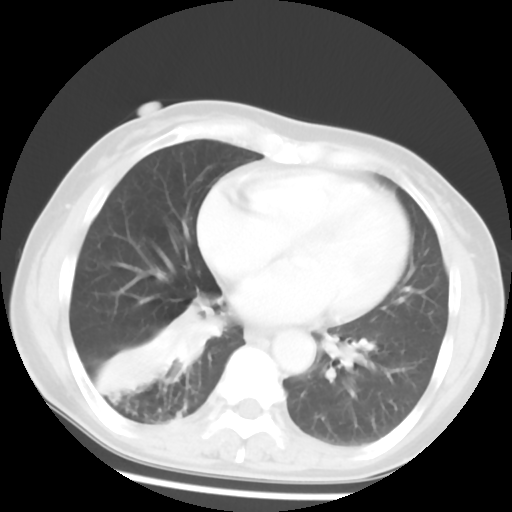
Chest CT, one axial slice; slice 22 of 52 in the series (ordered by position); lung window (W 1500 / L -600 HU); 5 mm slice thickness; 512 × 512 image matrix, field of view 297 × 297 mm. Patient: female, 54 years. From the clinical record (not read from this slice): clinical TNM (as recorded): T1c N0 M0.
Annotated regions visible in this slice (rectangle marked by the reading radiologist):
- lung tumour (recorded histology: squamous cell carcinoma): bounding box (x1, y1, x2, y2) in pixels: (167, 295, 223, 366)